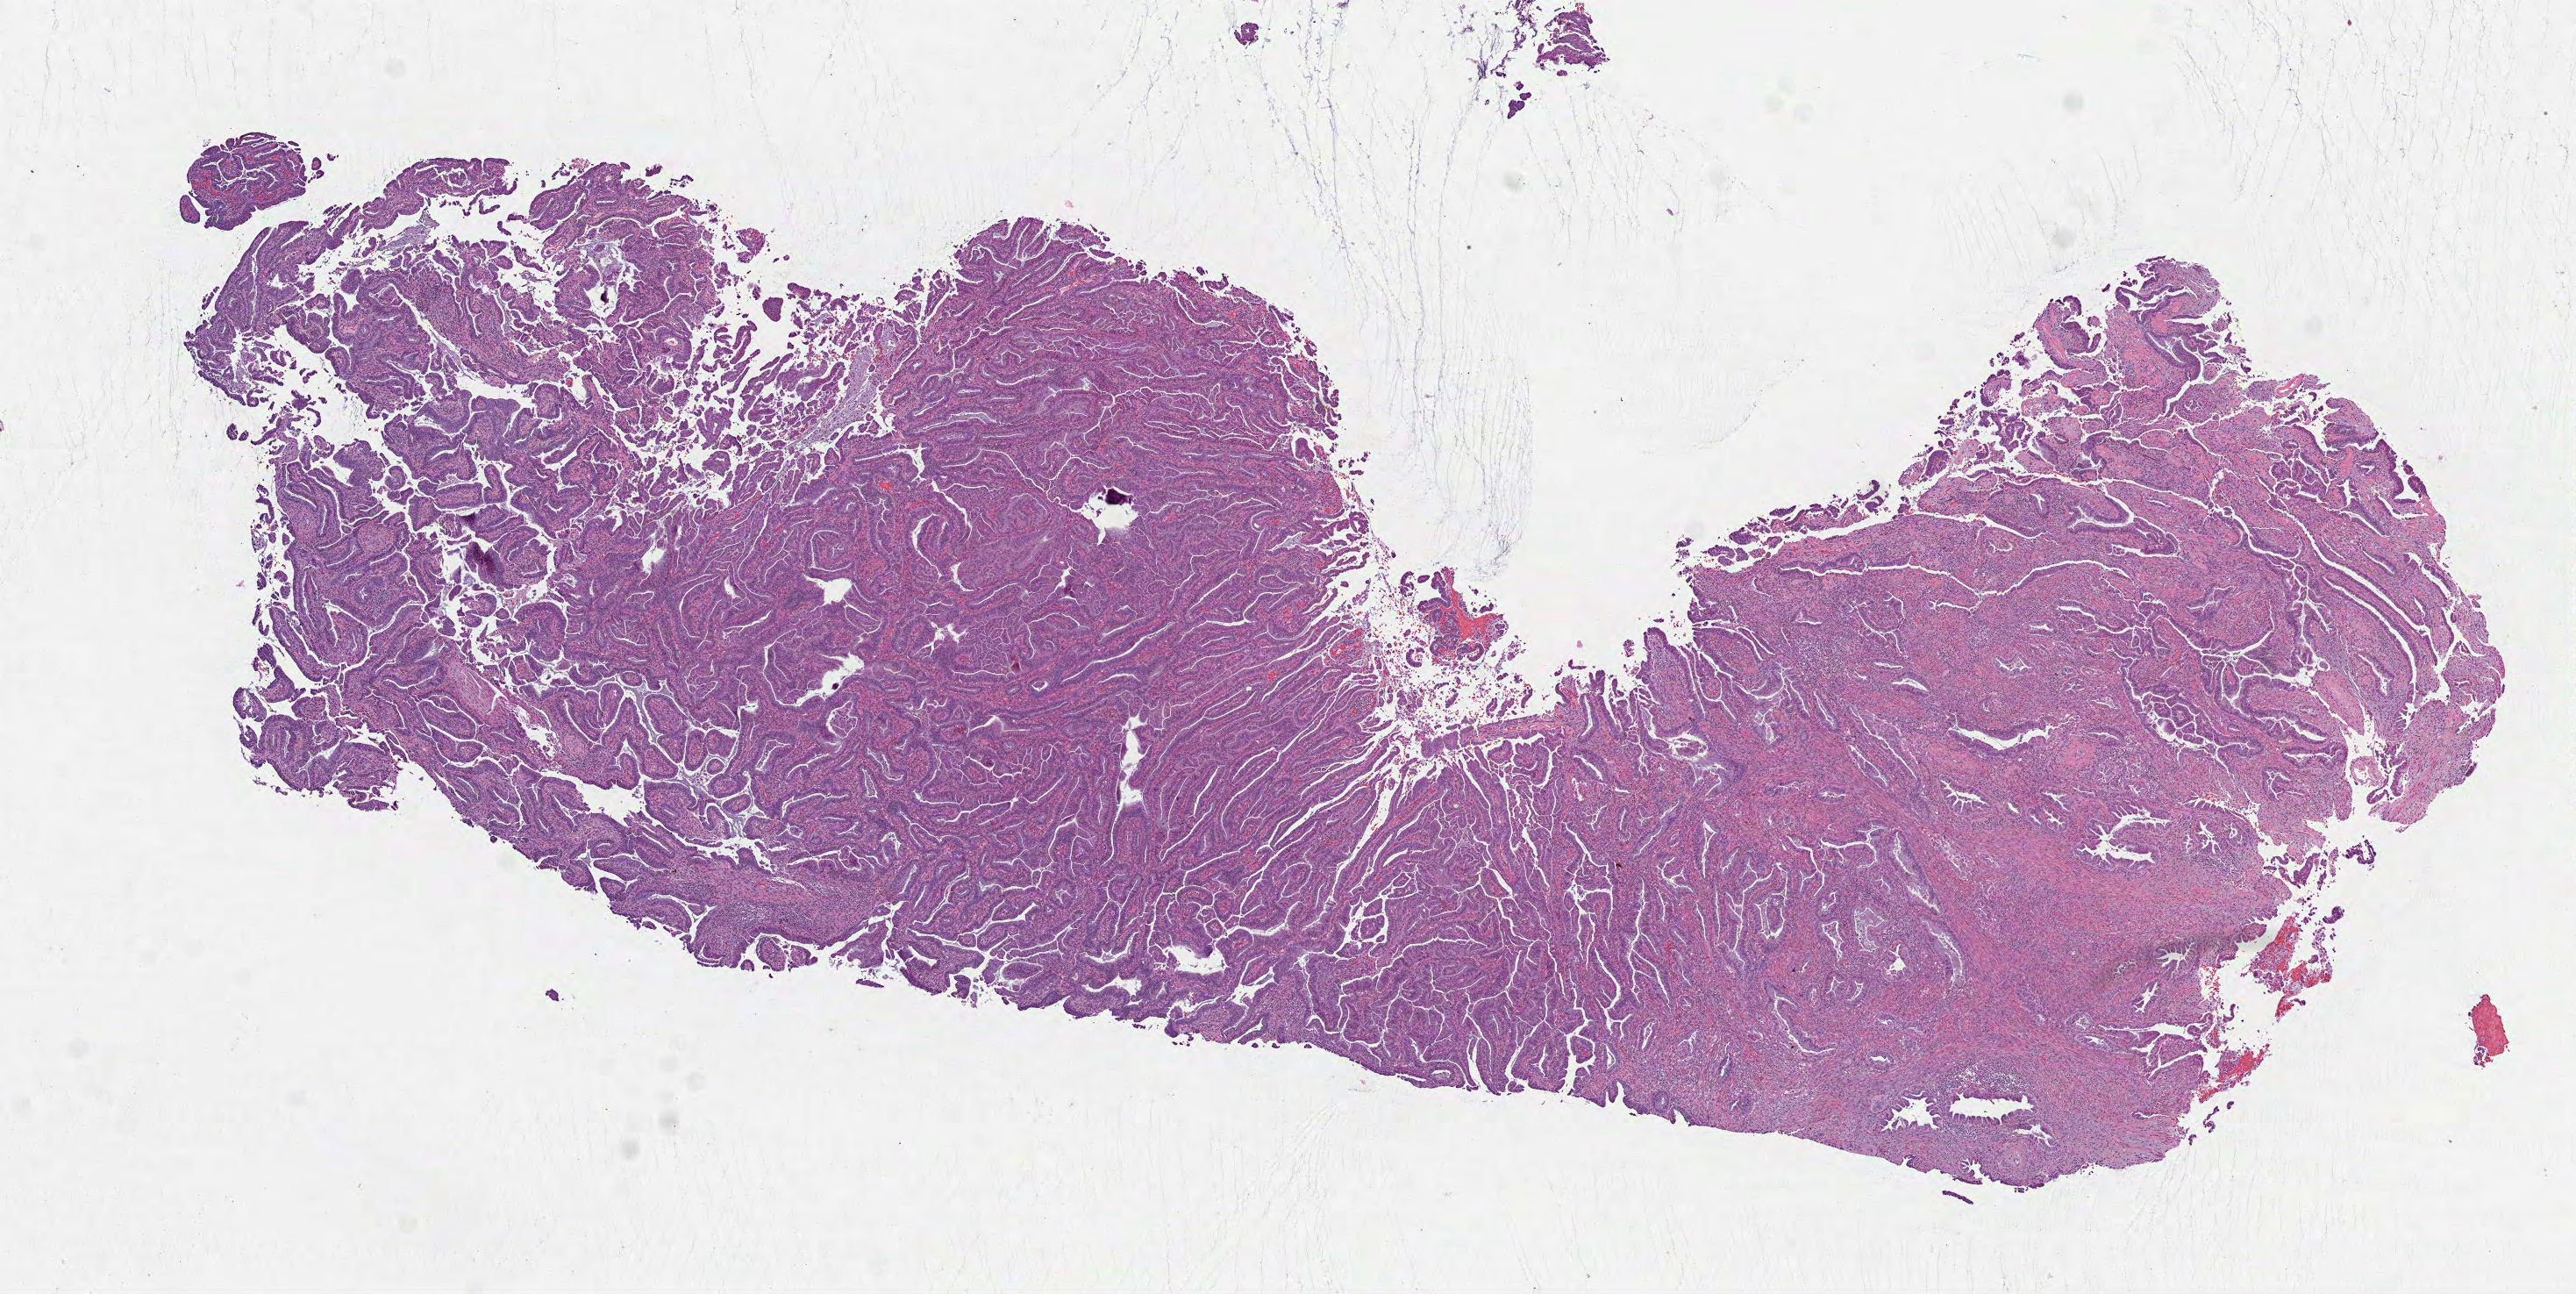
Digitized H&E-stained tissue section (whole slide), shown as a low-resolution overview of the whole scanned area (about 11.8 x 5.9 mm, from a 40x scan), formalin-fixed paraffin-embedded (FFPE) diagnostic section, cervix, primary tumour sample. Female, age 55 years at initial diagnosis. Histologic grade: G2 (moderately differentiated).
Diagnosis: Adenocarcinoma, NOS (cervix uteri). FIGO stage: IIB.